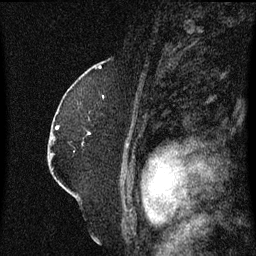
Breast MRI (dynamic contrast-enhanced), one sagittal slice; slice 44 of 60 in the series (ordered by position); dynamic contrast-enhanced series, image 2 of 3 at this slice position (ordered by acquisition); 1.5 T; TE 4.2 ms, TR 8.4 ms; 2 mm slice thickness; 256 × 256 image matrix. Female patient, age 52 years. From the clinical record (not read from this slice): setting: breast cancer imaged before/during neoadjuvant chemotherapy; receptor status: HR-positive, HER2-negative.
Annotated regions visible in this slice (semi-automatically segmented with operator editing):
- analysis volume of interest (the breast-tissue region the enhancement analysis was run in; not a lesion): box from (x=76, y=104) to (x=92, y=147) px
- tumour enhancement mask (voxels above the 70 % enhancement threshold inside the analysis volume of interest): (x=89, y=132)–(x=91, y=135)